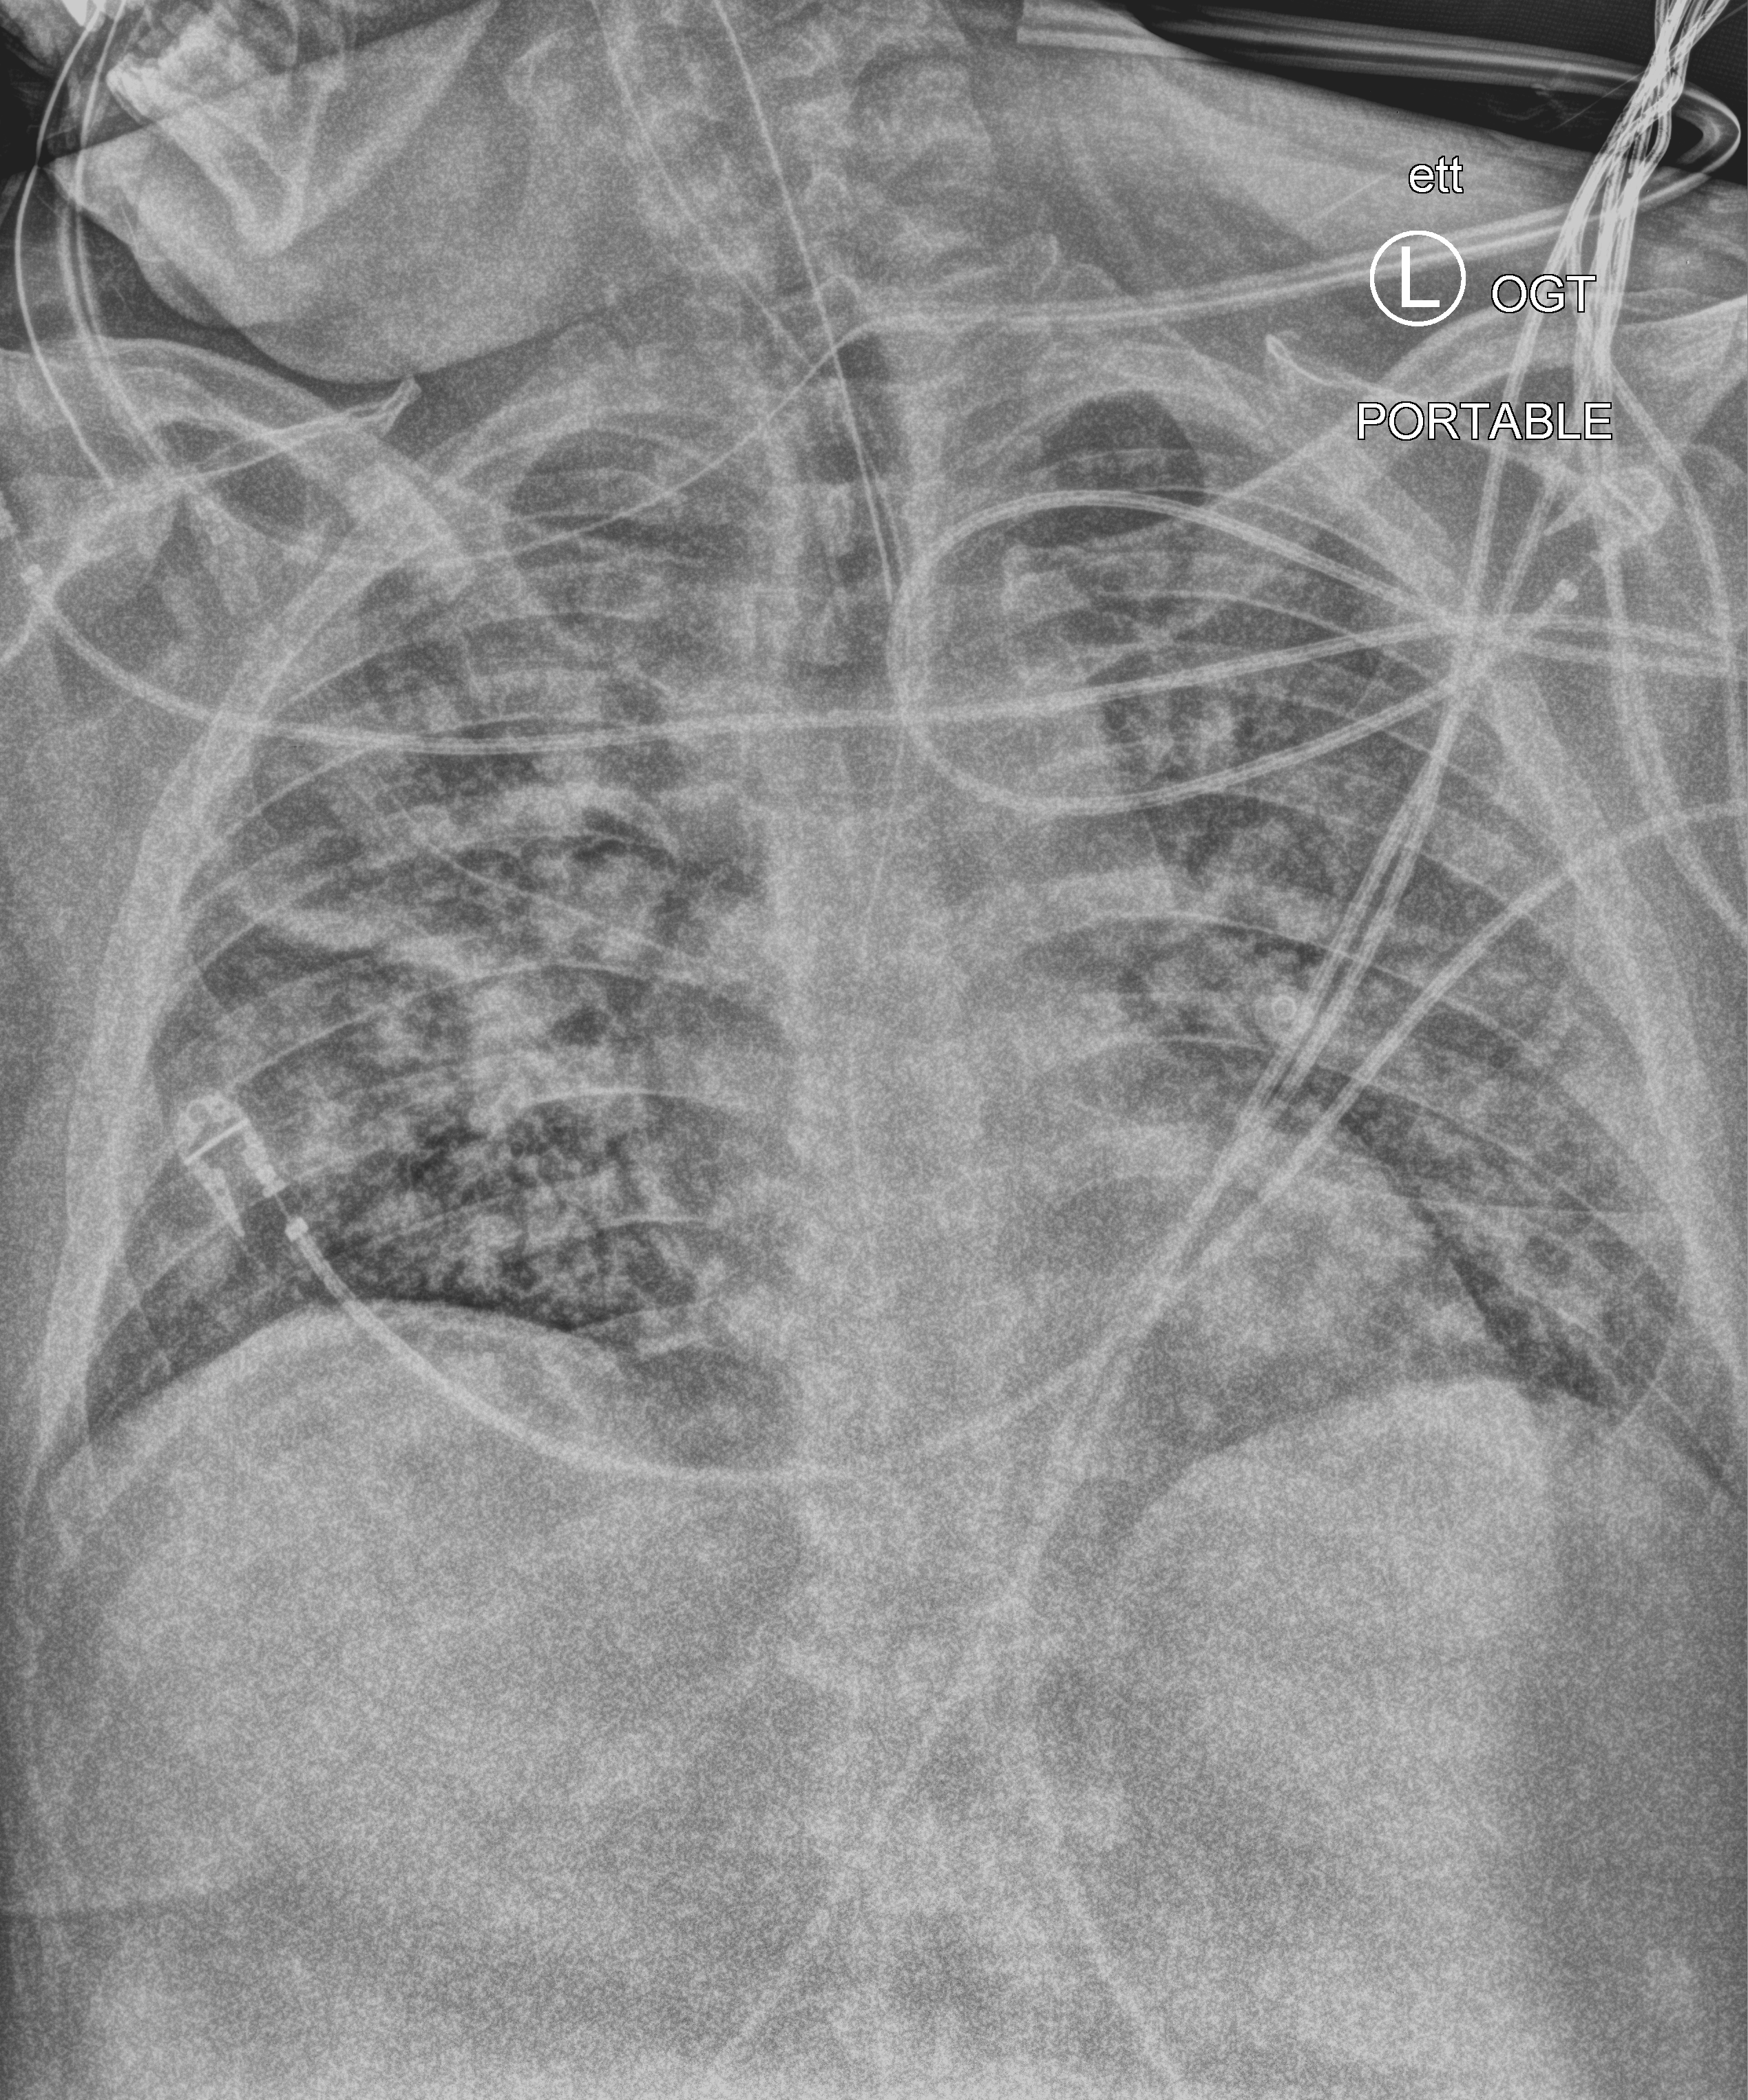
Portable chest radiograph, anteroposterior (AP) projection. Patient hospitalised with COVID-19, aged 18–59 years.
Hospital-stay facts (about this admission, not read from this image; timing relative to this image not recorded):
- mechanically ventilated during this hospital stay: yes
- admitted to intensive care during this hospital stay: yes